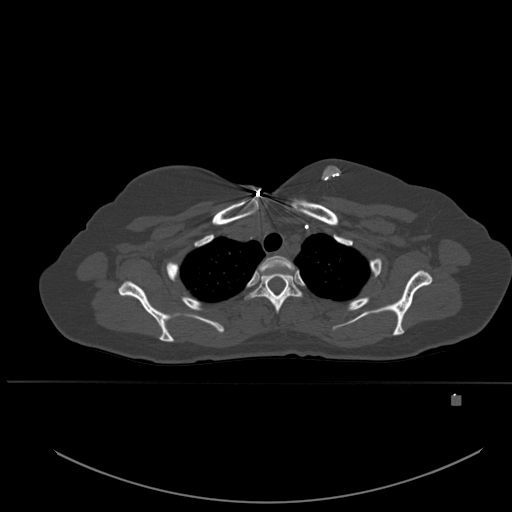
CT including the spine, one axial slice. Bone window (W 1800 / L 400 HU). 1.5 mm slice thickness. 512 × 512 image matrix, field of view 443 × 443 mm. Patient: female, 49 years. From the clinical record (not read from this slice): primary cancer: breast.
Outlined on this slice (semi-automatically segmented with operator editing):
- T1 vertebra: bounding box <257,256,296,277> (left, top, right, bottom; pixels)
- T2 vertebra: <247,269,302,314>